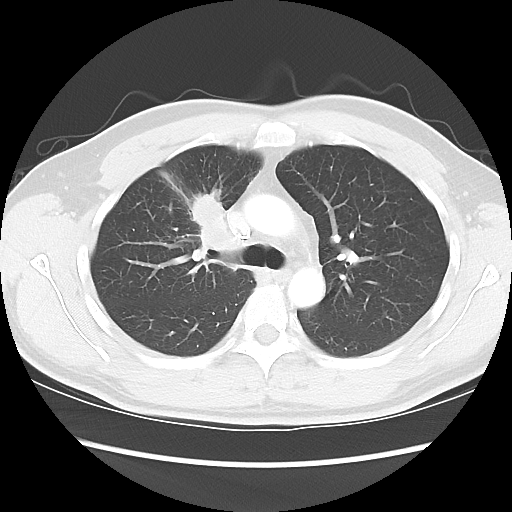
Chest CT, one axial slice; slice 62 of 80 in the series (ordered by position); reconstruction kernel LUNG; 120 kVp; lung window (W 1500 / L -600 HU); 5 mm slice thickness; 512 × 512 image matrix, field of view 360 × 360 mm. Patient: male, 35 years. From the clinical record (not read from this slice): clinical TNM (as recorded): T1c N1 M1b.
Structures marked on this image (bounding box drawn by a radiologist):
- lung tumour (recorded histology: adenocarcinoma): box from (x=181, y=190) to (x=240, y=259) px